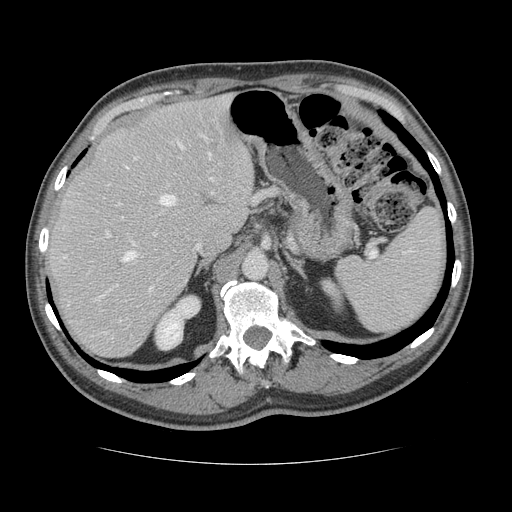
Contrast-enhanced abdominal CT, one axial slice. Position 90 of 134 along the scan axis. Reconstruction kernel STANDARD. 120 kVp. Soft-tissue window (W 400 / L 40 HU). 512 × 512 image matrix, field of view 377 × 377 mm. Male patient, age 68 years. Case-level facts recorded for this patient, not image findings: diagnosis: colorectal cancer liver metastases, imaged before liver resection.
Outlined on this slice (manually delineated by an expert):
- hepatic veins: bounding box (x1, y1, x2, y2) in pixels: (123, 136, 213, 261)
- liver: (47, 97, 254, 358)
- planned liver remnant (the part of the liver to remain after resection): (47, 97, 254, 336)
- portal vein (with intrahepatic branches): (106, 140, 215, 291)